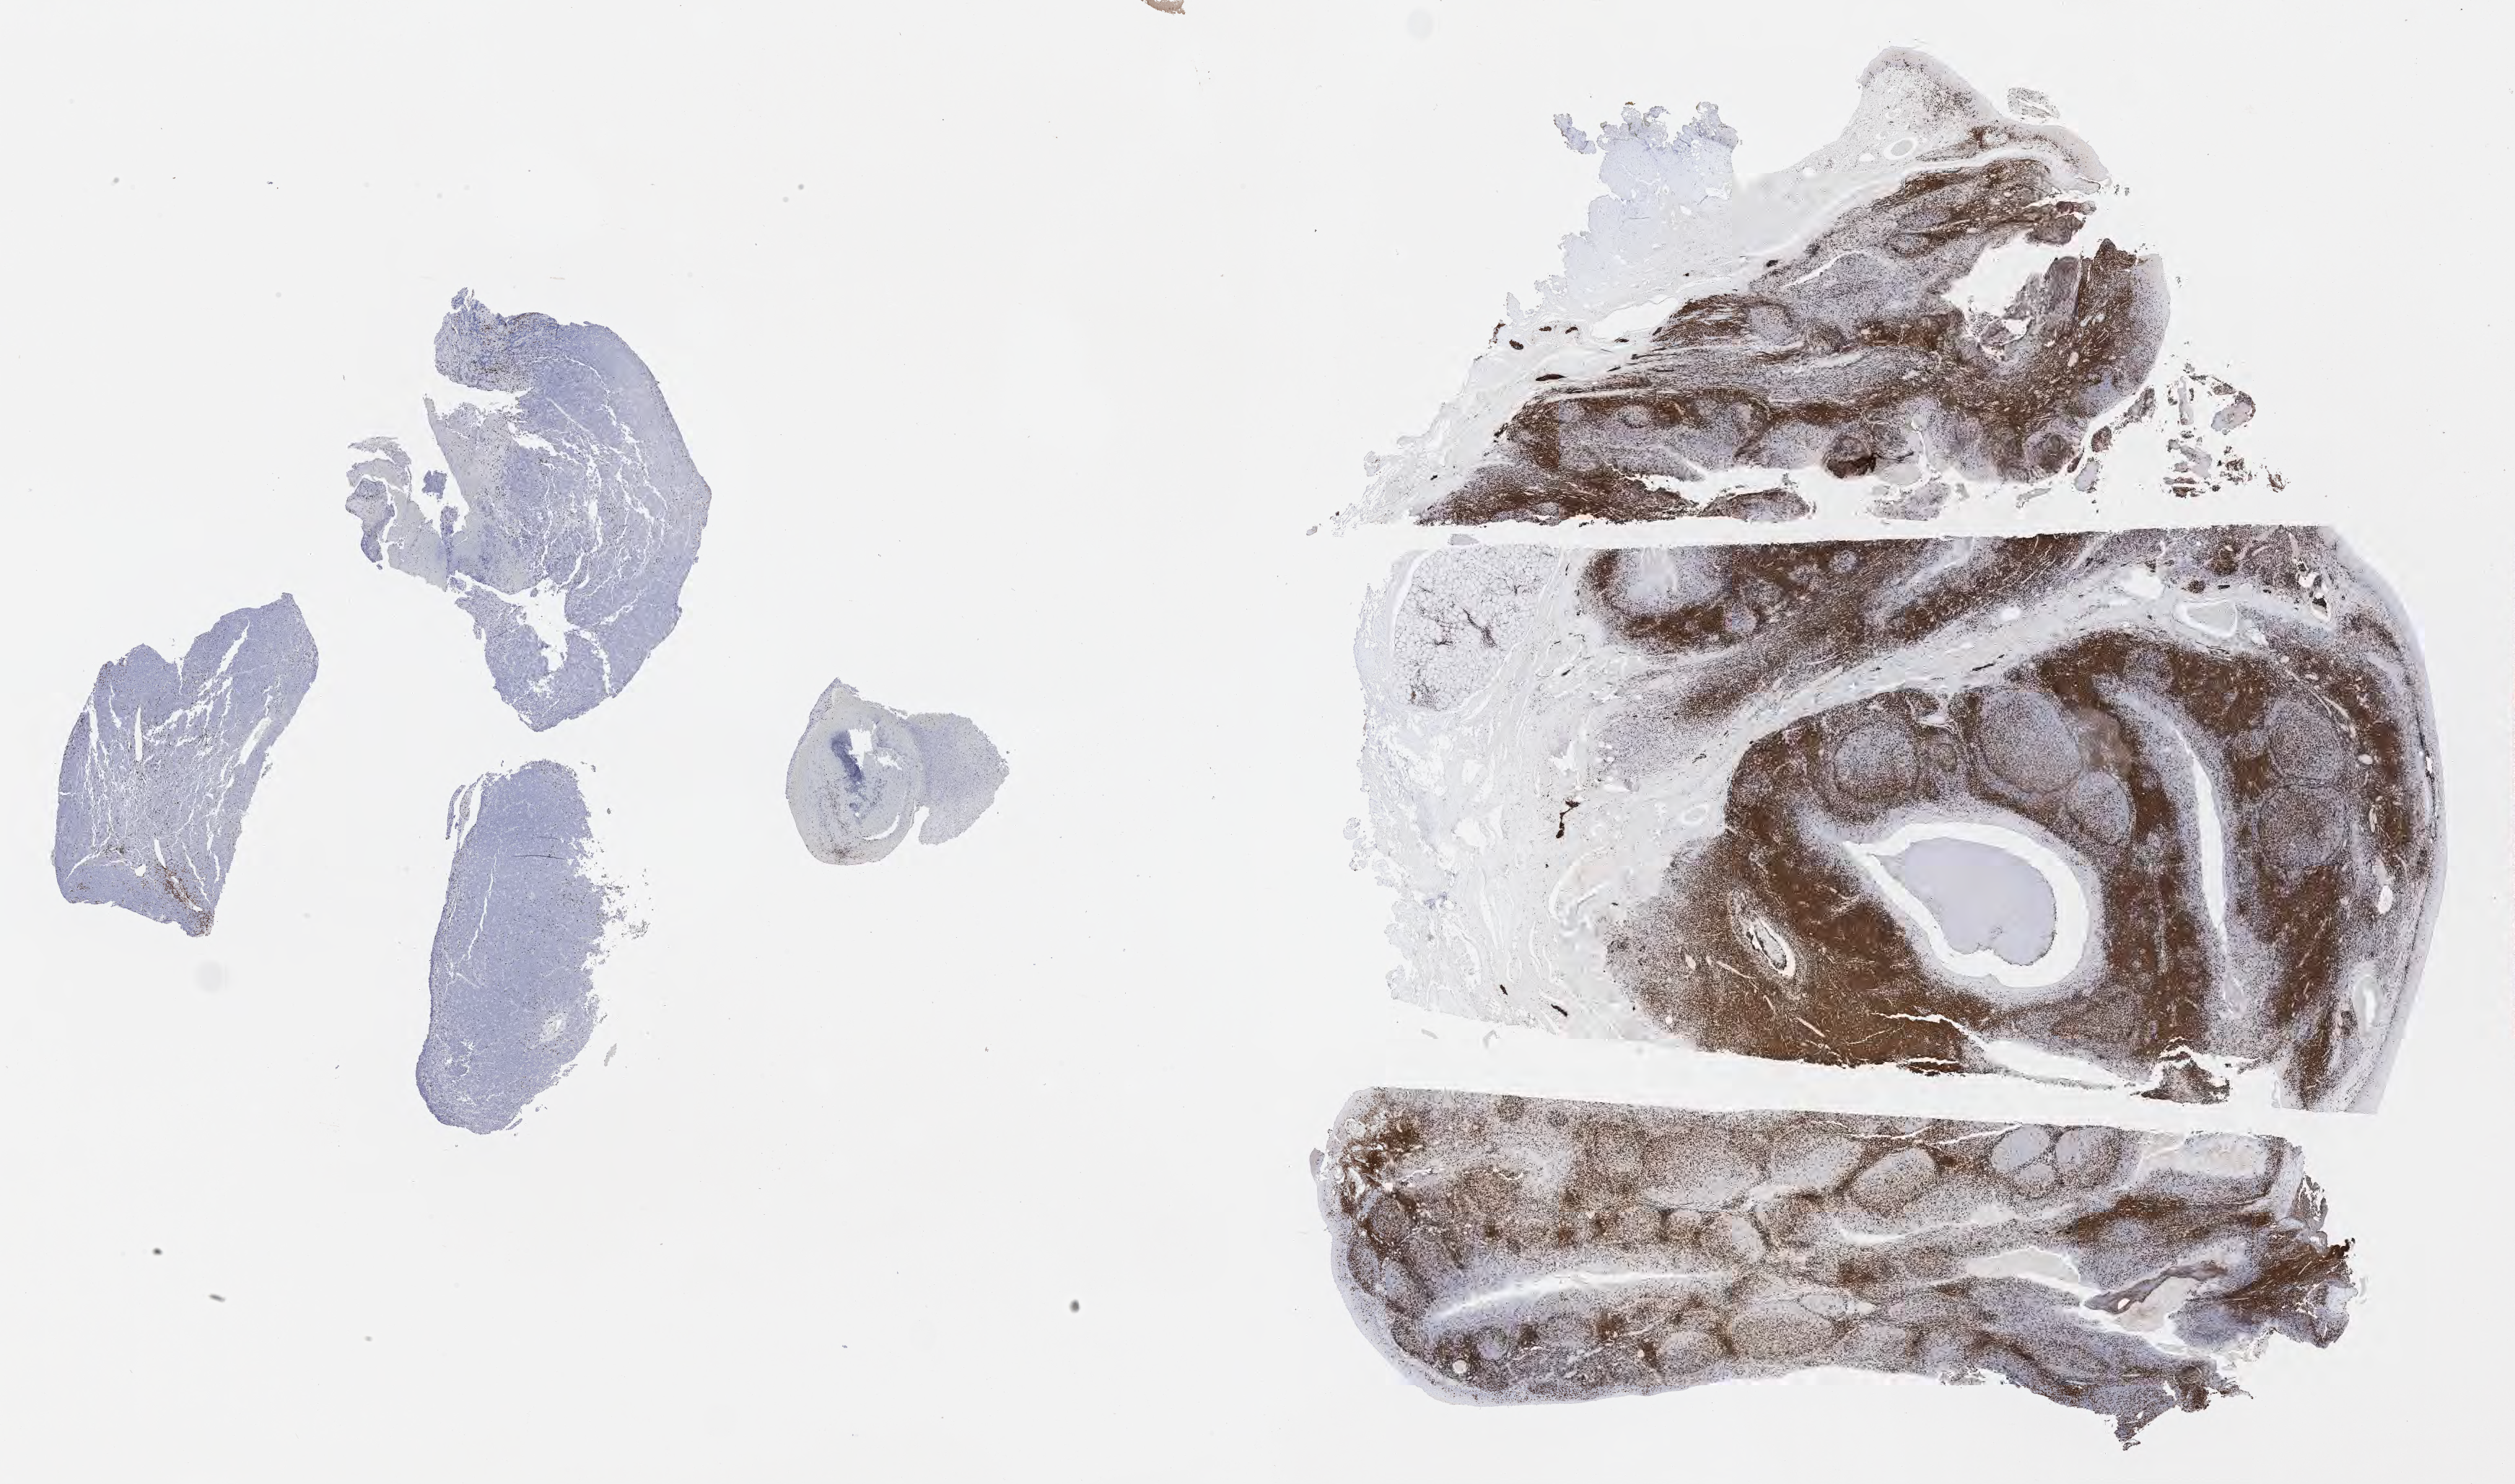
Immunohistochemistry (IHC) whole-slide image stained for CD3 — low-resolution overview of the scanned area, about 28.2 x 16.6 mm. Specimen: tumor tissue. Male patient, aged 10.
Diagnosis: Burkitt lymphoma, NOS.